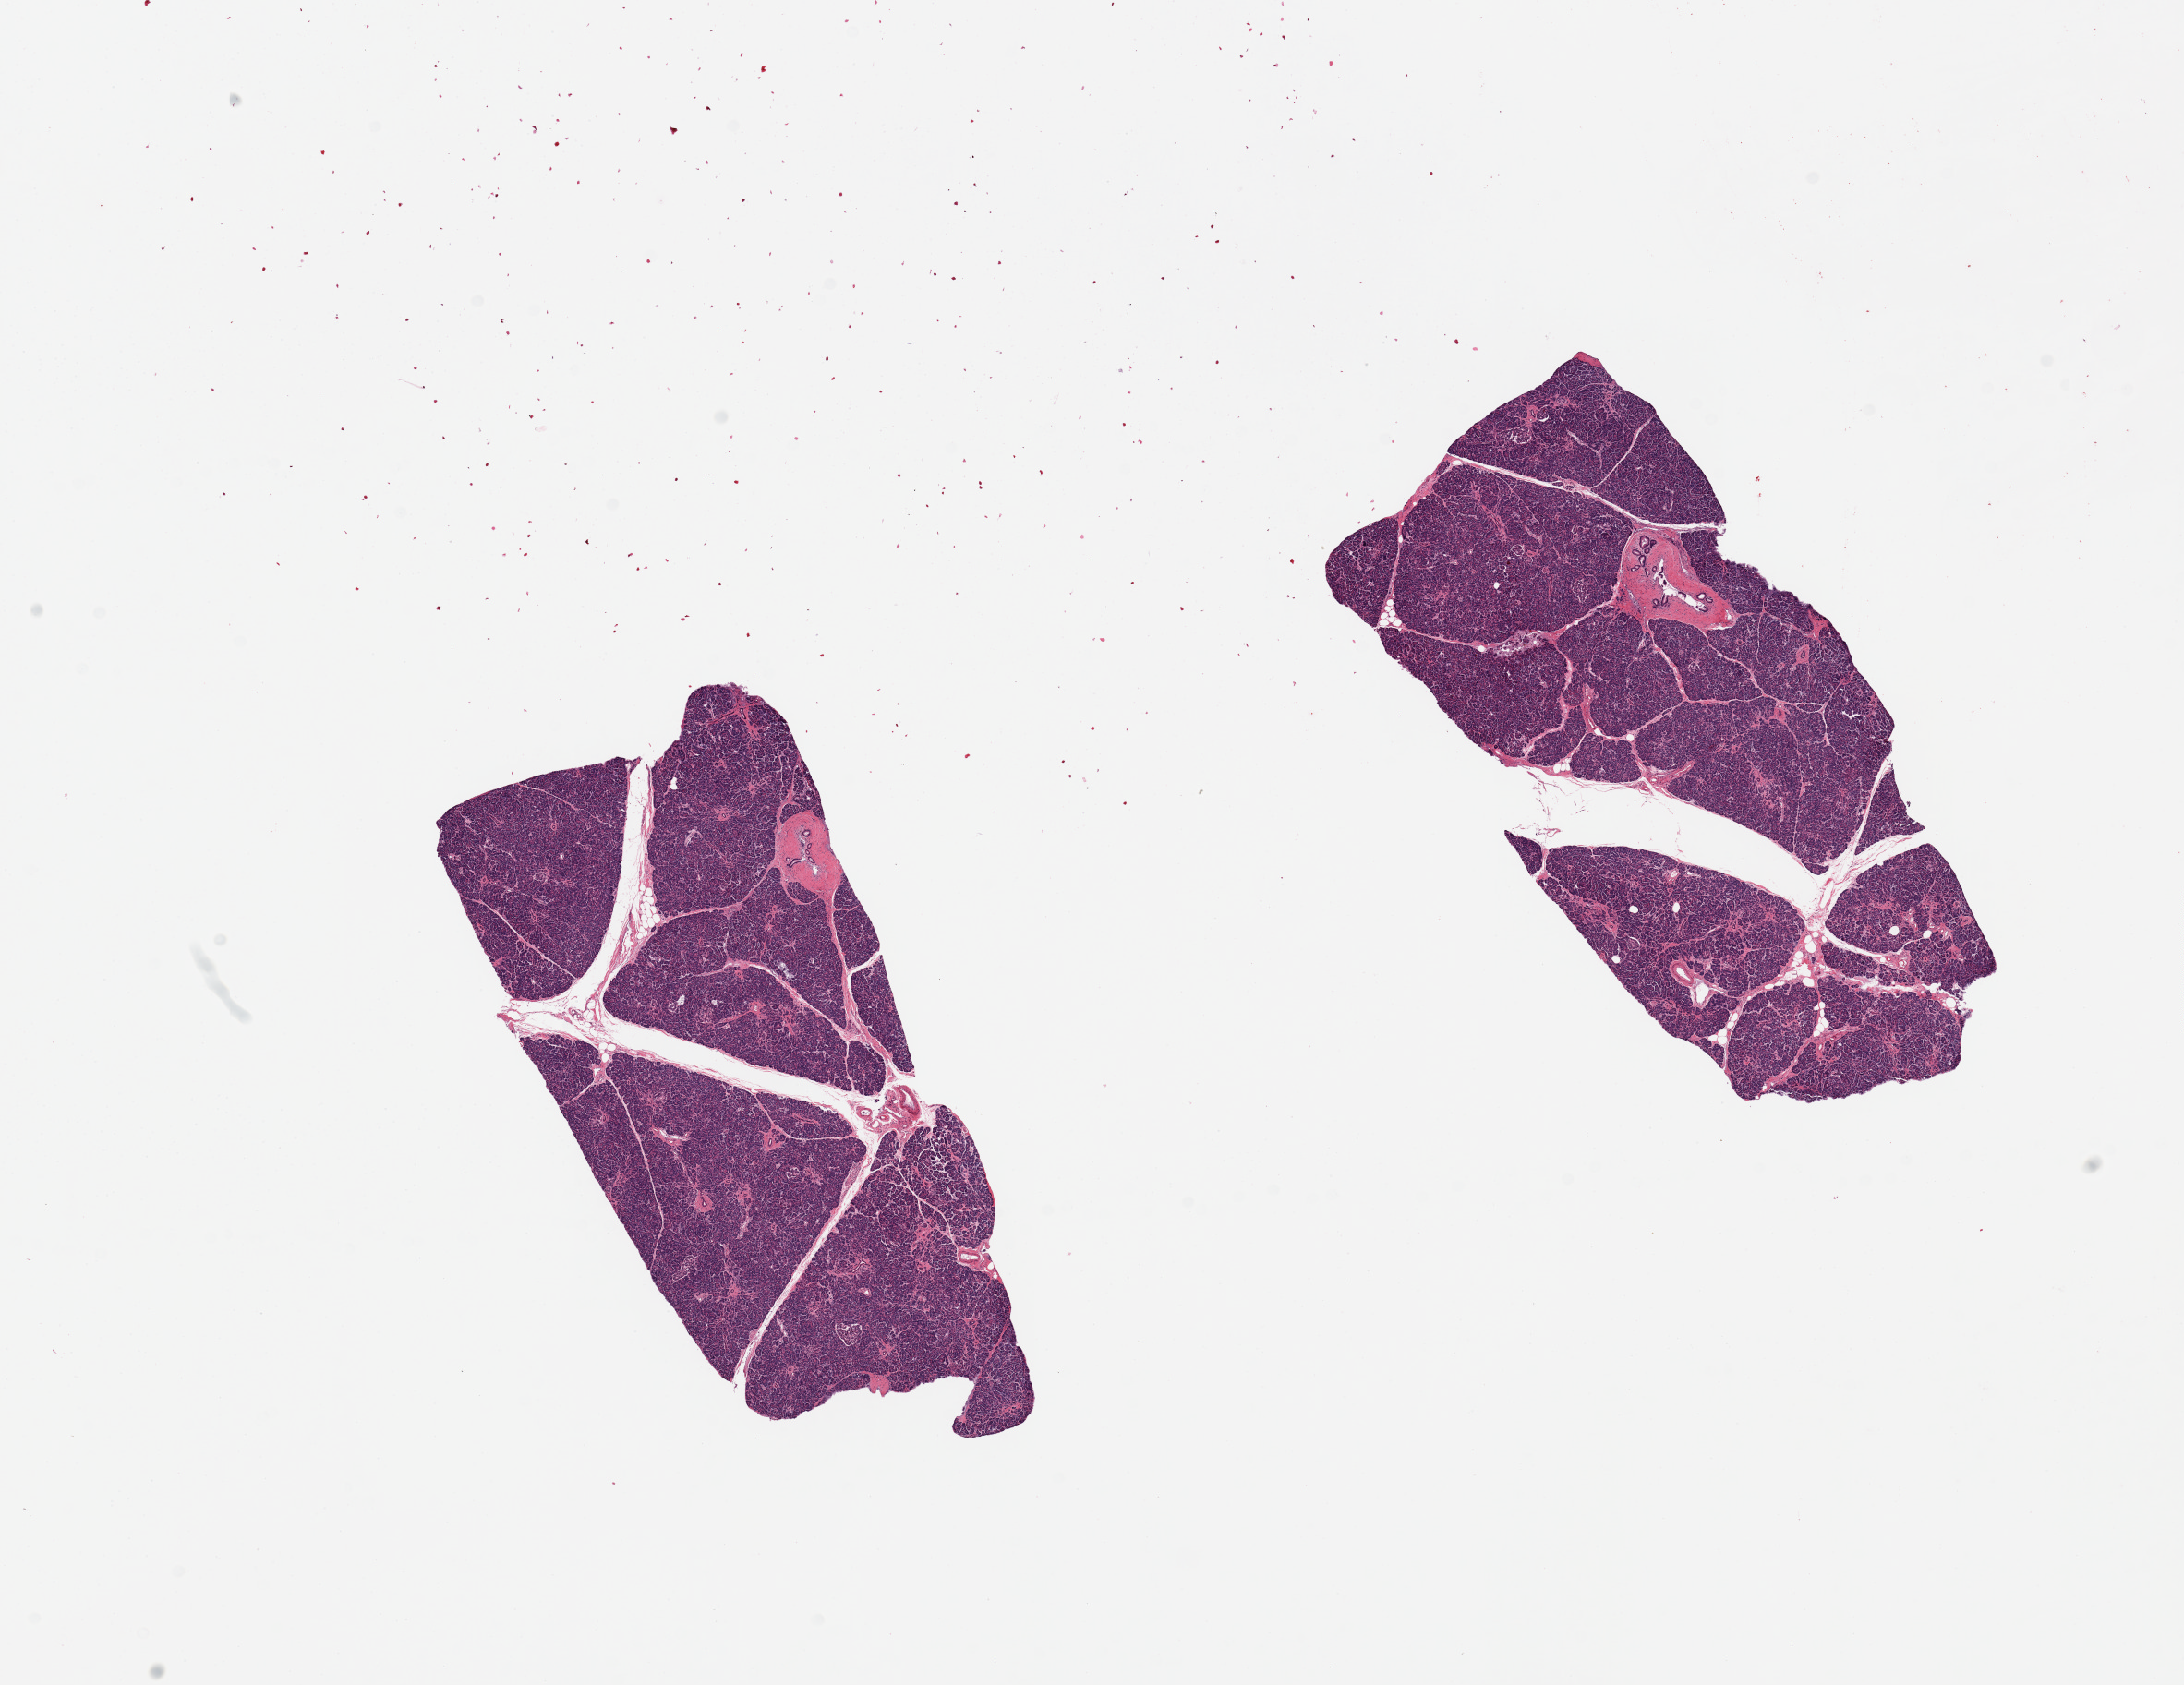
Haematoxylin and eosin whole-slide image — shown as a low-resolution overview of the whole scanned area (about 18.7 x 14.4 mm, acquisition: 20x scan); PAXgene-fixed paraffin-embedded (PFPE) section; target tissue: pancreas; donor tissue sample. Male donor.
- review note (as recorded): 2 pieces, extremely well-preserved; Islets well- visualized